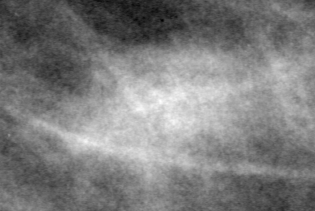
Cropped region of a digitized screen-film mammogram centred on a radiologist-marked abnormality, right breast, MLO view.
Marked abnormality: mass, shape focal asymmetric density, margins ill defined; BI-RADS assessment category 4; subtlety rating 2 on a 1 (subtle) to 5 (obvious) scale; pathology result (as recorded, not read from the image): malignant.